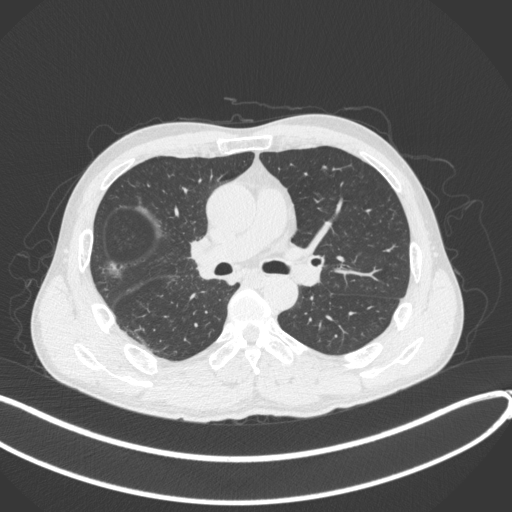
Chest CT, one axial slice; position 227 of 409 along the scan axis; reconstruction kernel B31f; 120 kVp; lung window (W 1500 / L -600 HU); 512 × 512 image matrix. Male patient, age 53 years. From the clinical record (not read from this slice): clinical TNM (as recorded): T1b N0 M0.
Annotated regions visible in this slice (bounding box drawn by a radiologist):
- lung tumour (recorded histology: squamous cell carcinoma): bounding box (x1, y1, x2, y2) in pixels: (183, 233, 219, 292)